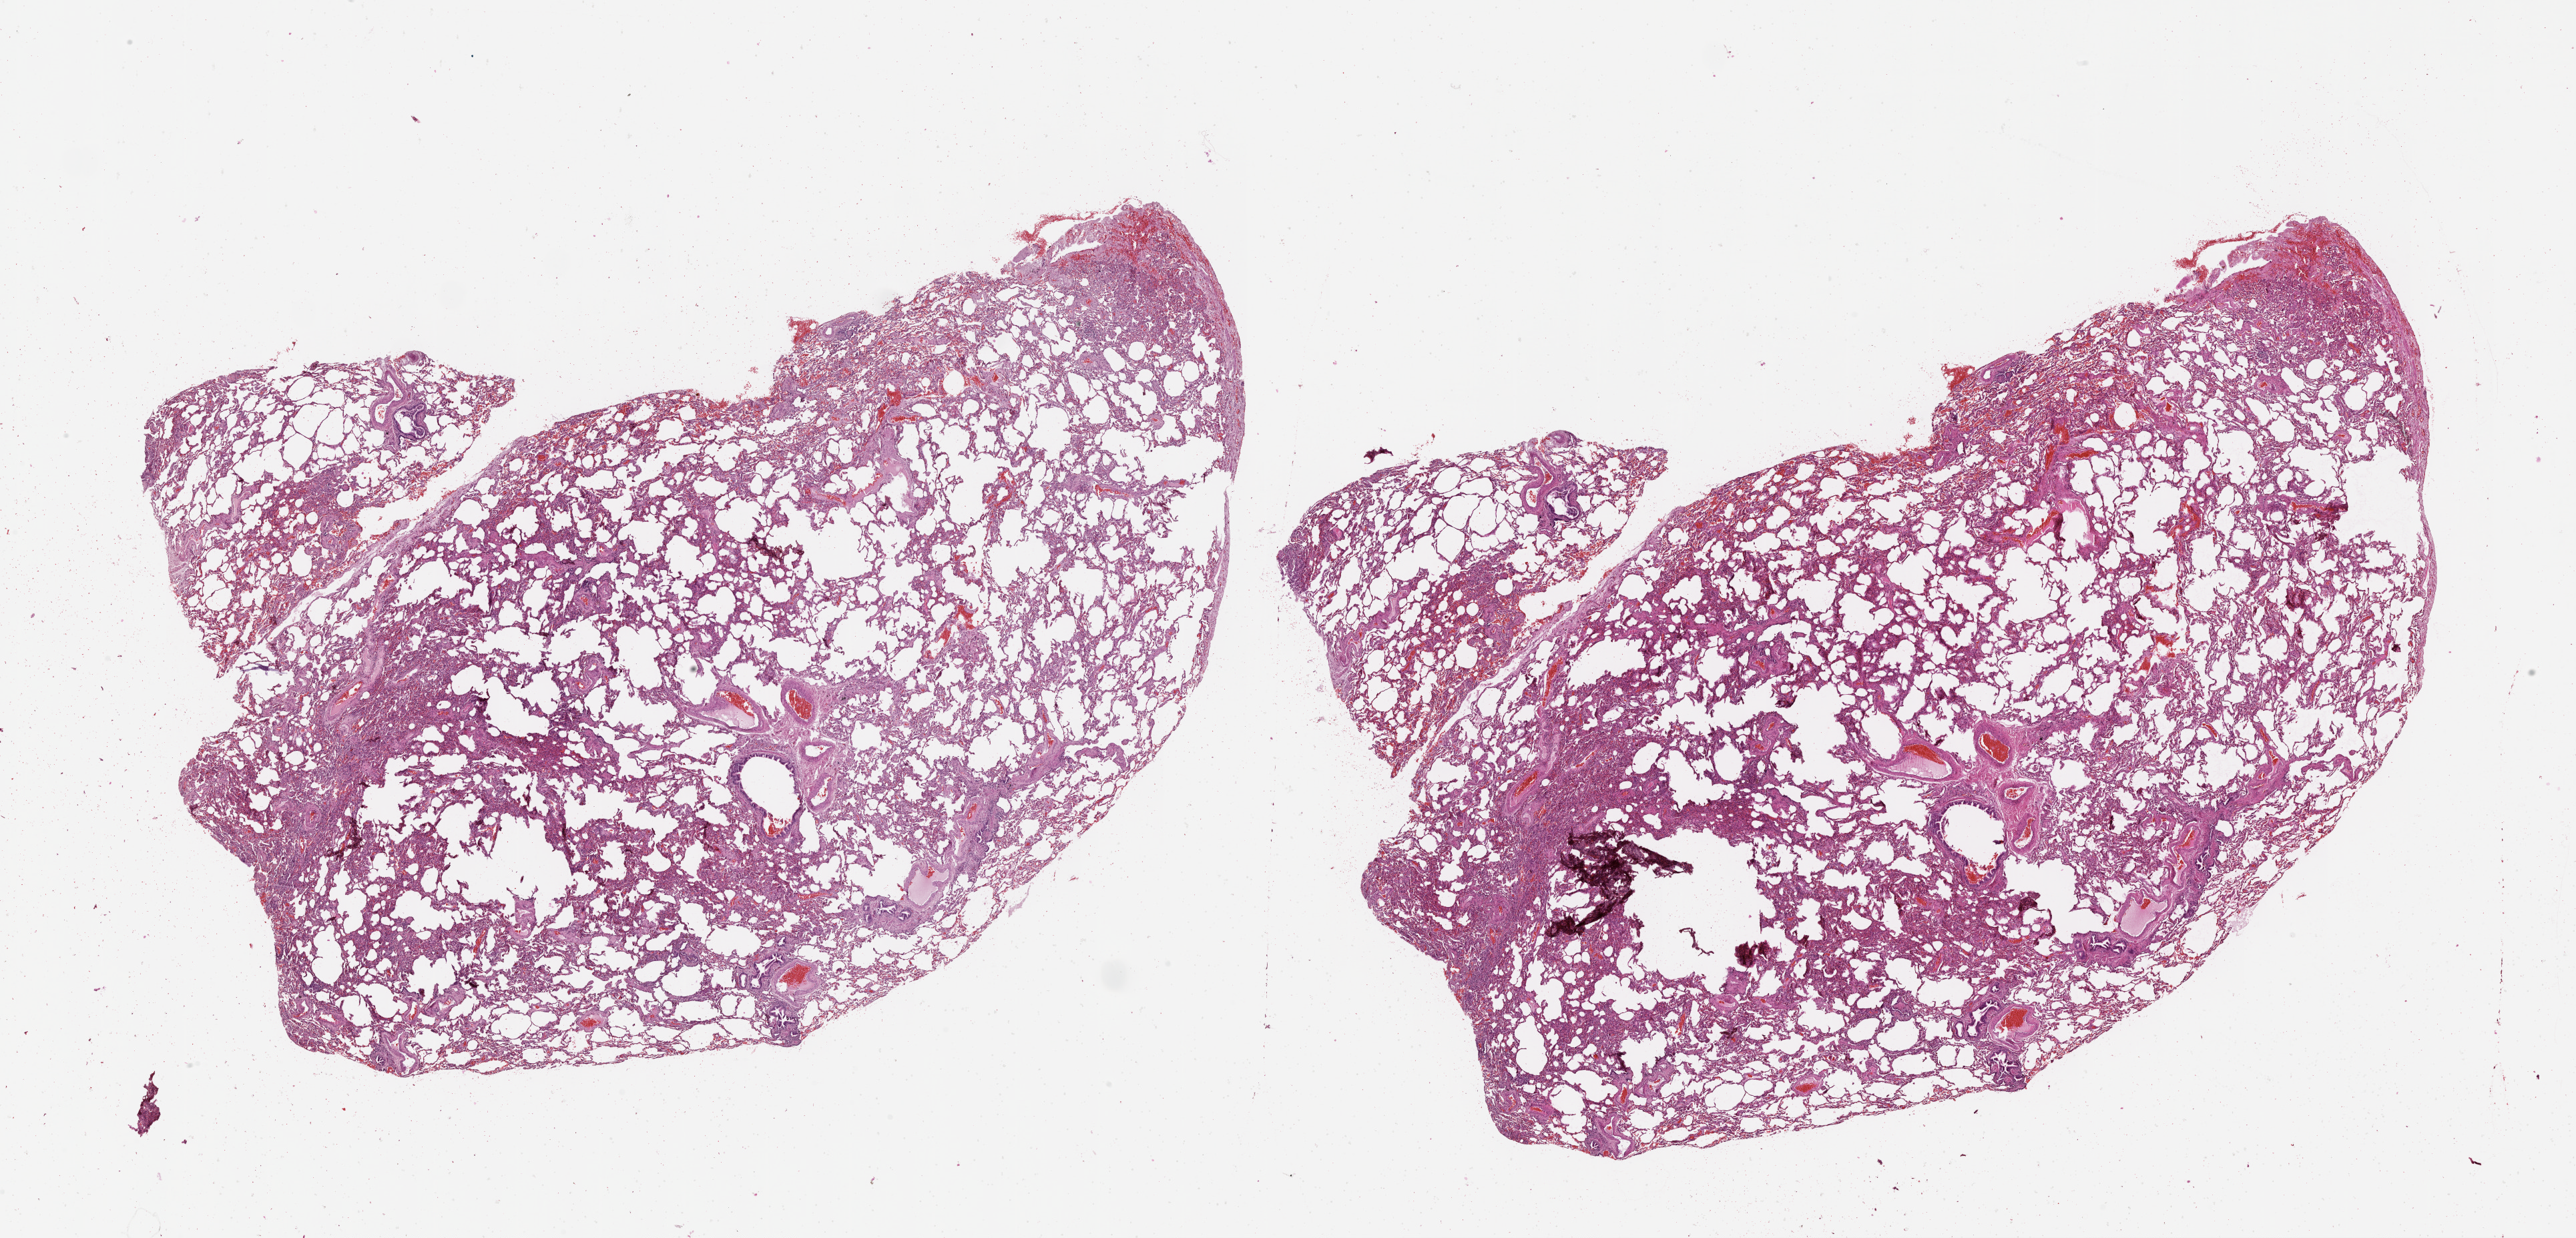
Digitized H&E-stained tissue section (whole slide) — shown as a low-resolution overview of the whole scanned area (about 31.1 x 14.9 mm, slide scanned at 20x), lung, normal (non-tumour) tissue. 62-year-old female patient.
This section: normal (non-tumour) tissue from the same patient. Patient diagnosis (cohort enrolment): squamous cell carcinoma (lung).